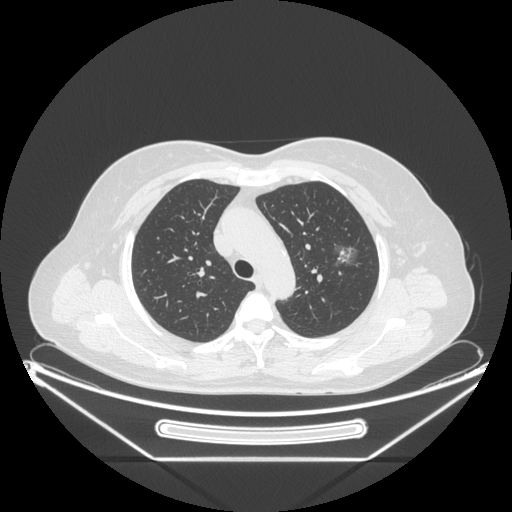
Chest CT, one axial slice; position 159 of 226 along the scan axis; lung window (W 1500 / L -600 HU); 512 × 512 image matrix, field of view 447 × 447 mm. Patient: female, 54 years. Case-level facts recorded for this patient, not image findings: clinical TNM (as recorded): T1c N0 M0; histopathological grade: G1.
Annotated regions visible in this slice (rectangle marked by the reading radiologist):
- lung tumour (recorded histology: adenocarcinoma): box from (x=325, y=235) to (x=363, y=272) px